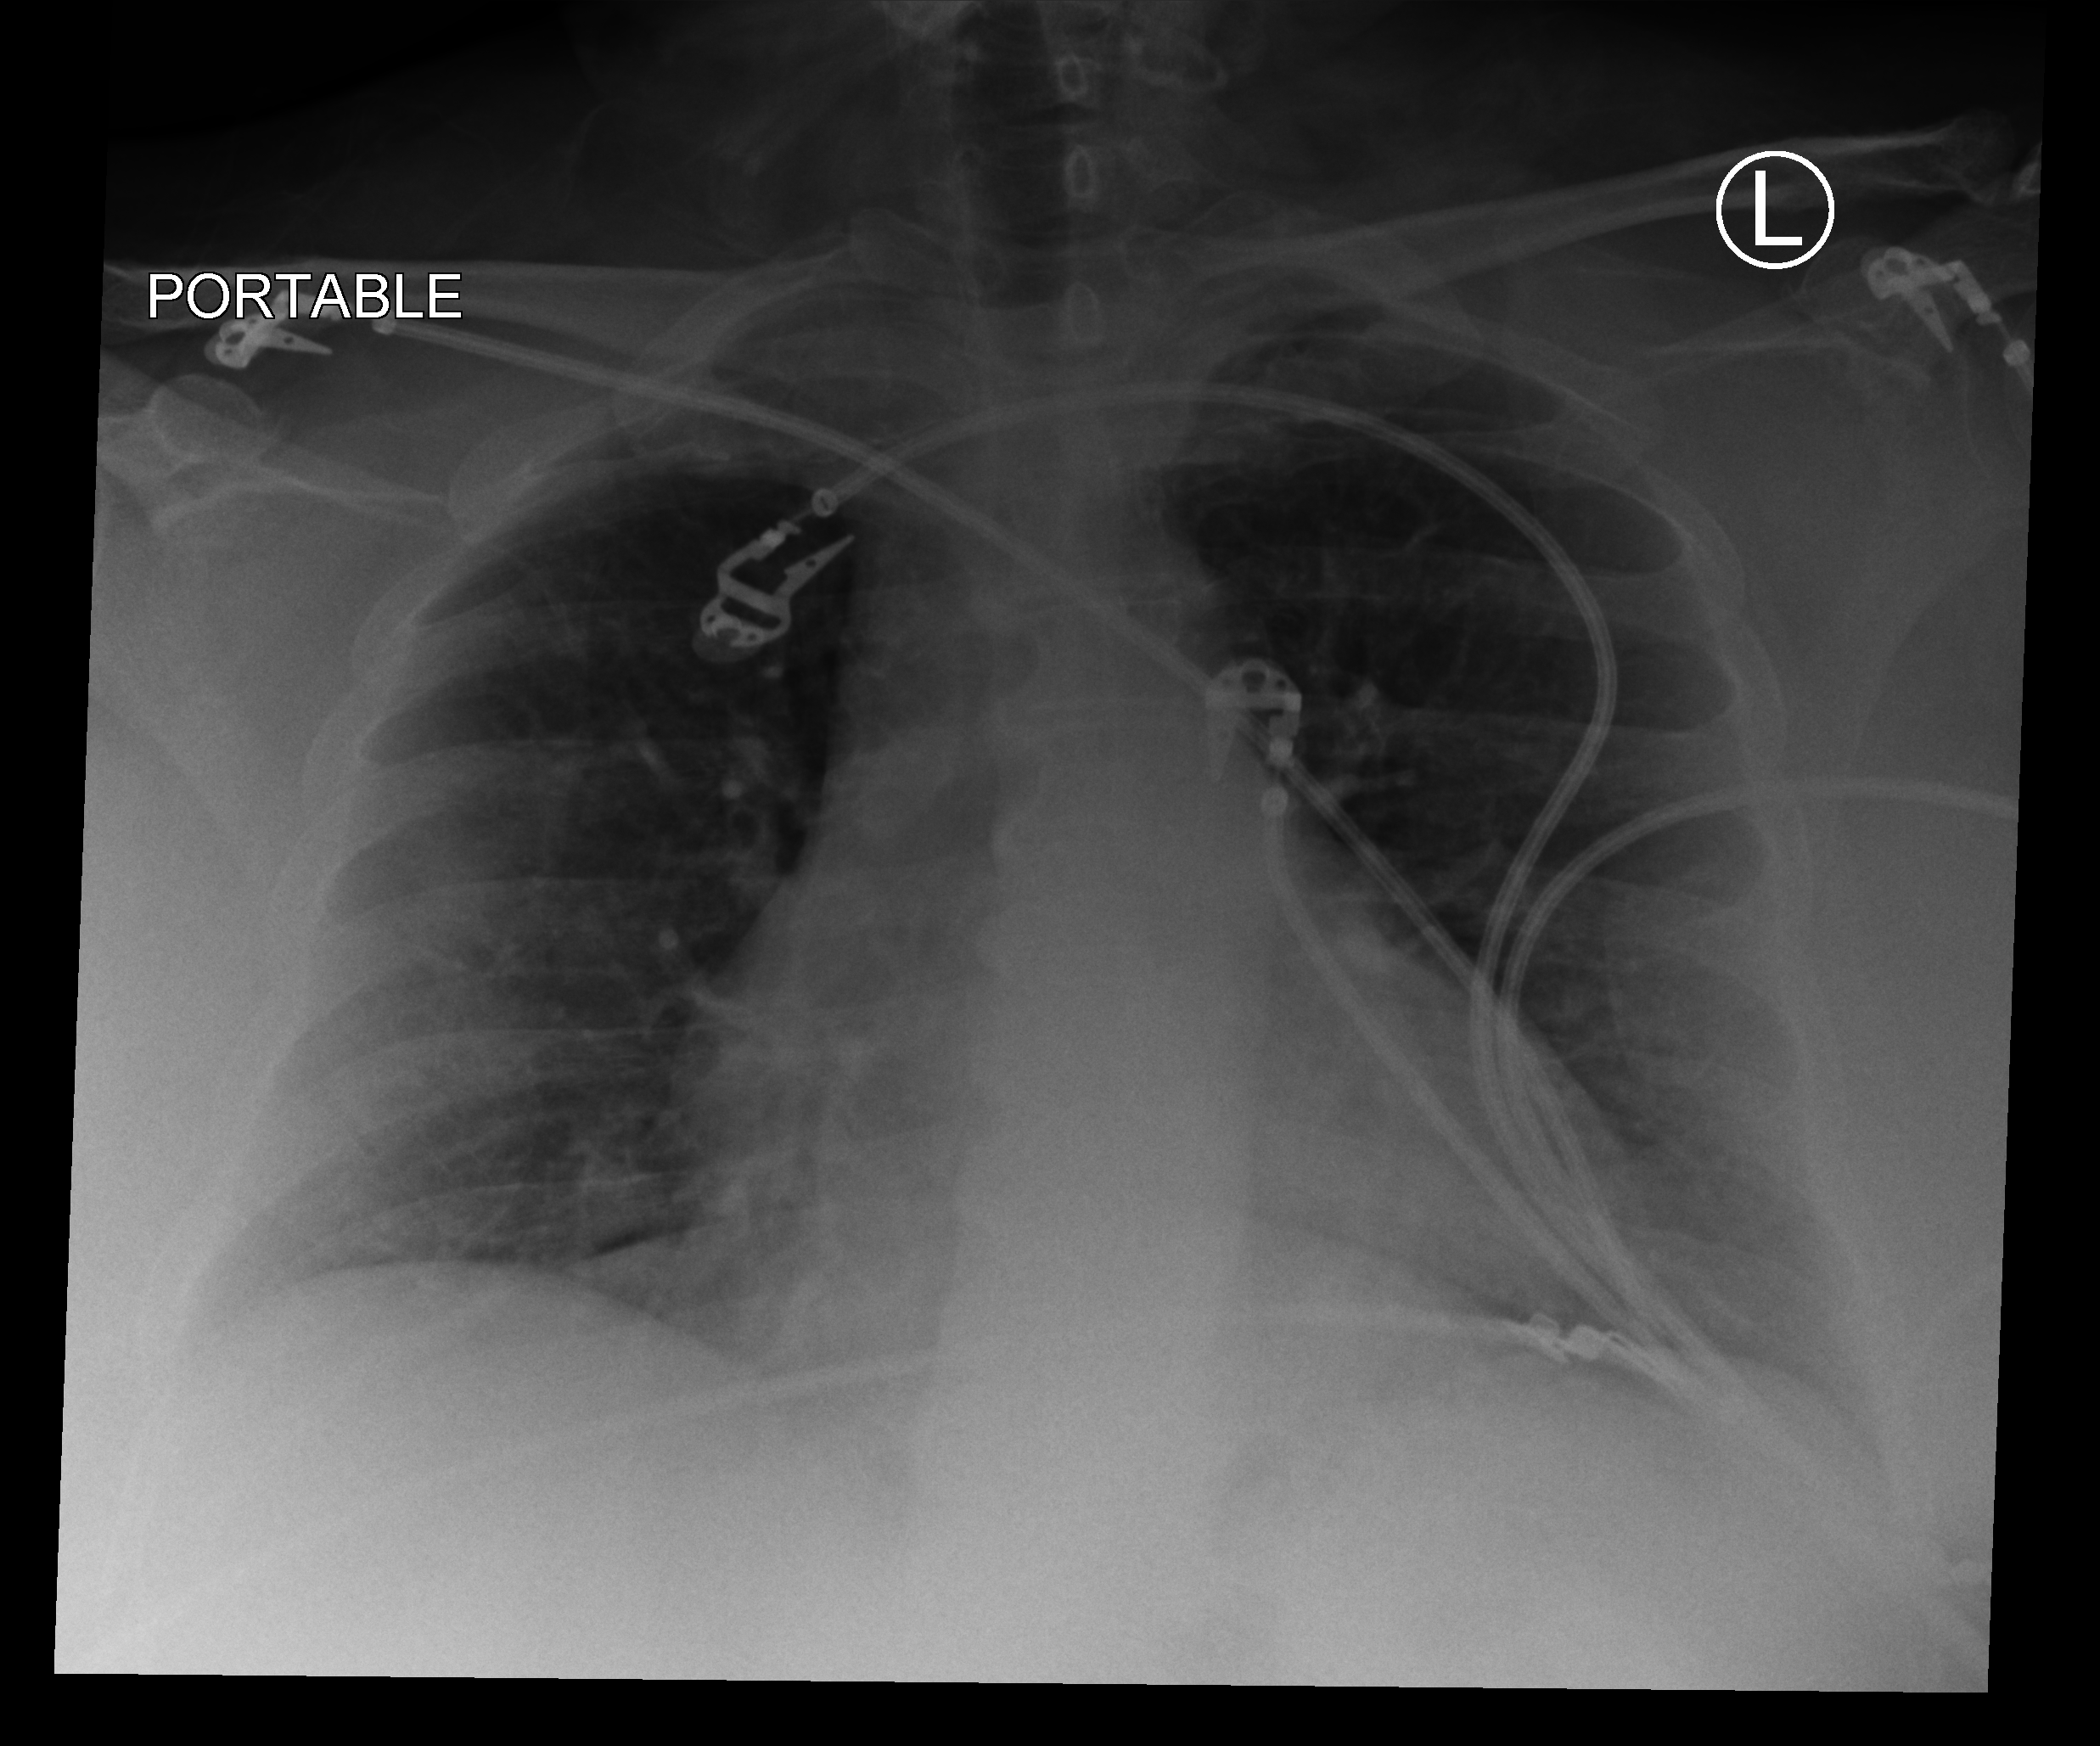
Portable chest radiograph, anteroposterior (AP) projection. Patient hospitalised with COVID-19; female, aged 18–59 years.
From the hospital-stay record, not from the radiograph (when in the stay this image was taken is not recorded): mechanically ventilated during this hospital stay: no; admitted to intensive care during this hospital stay: no; smoking status (admission record): never.